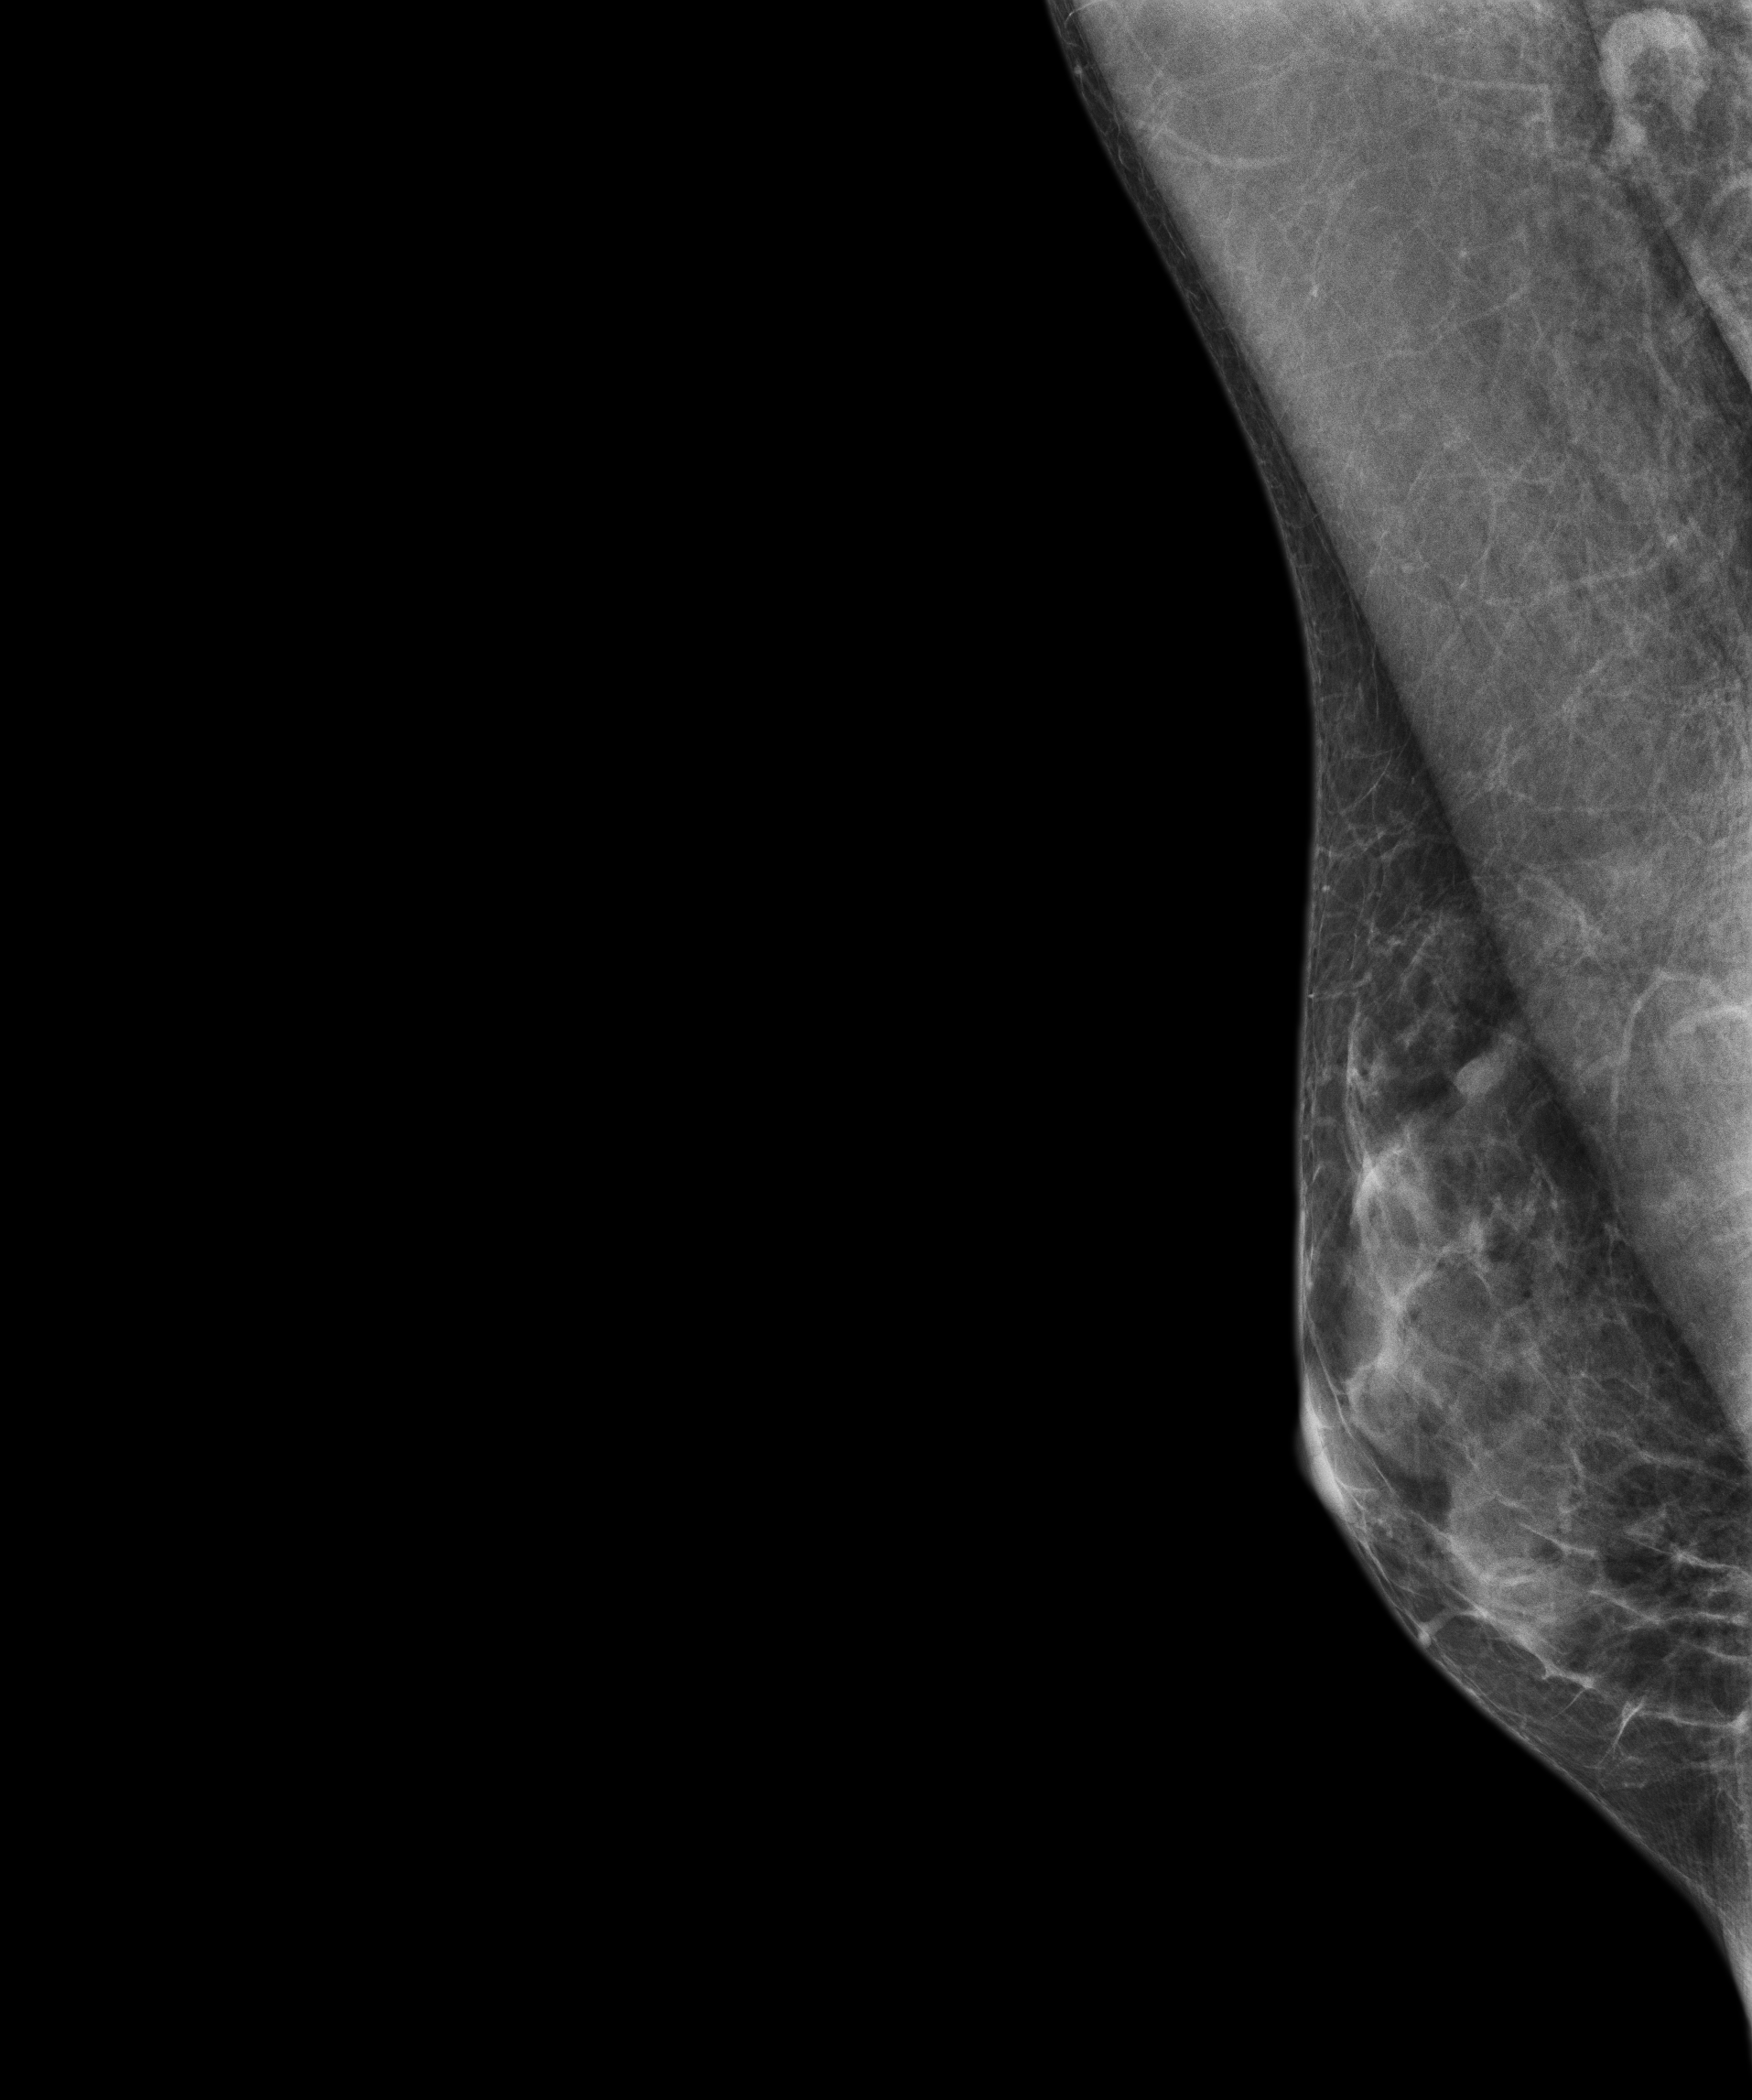
Digital mammogram (FFDM), right breast, MLO view, annual screening mammography examination, compressed breast thickness 29 mm, system: Senographe Essential ADS_56.21.3. Female patient, age 55 years.
- breast density at the screening exam (both breasts): extremely dense (BI-RADS density category d)
- final BI-RADS category for the screening round (tomosynthesis exam, both breasts): category 1
- recall: no recall after this screen